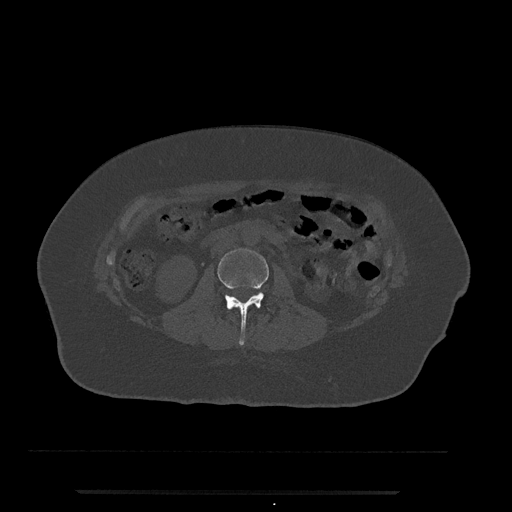
CT including the spine, one axial slice. Slice 30 of 797 in the series (ordered by position). Reconstruction kernel Br40s/3. 120 kVp. Bone window (W 1800 / L 400 HU). 512 × 512 image matrix, field of view 440 × 440 mm. Female patient, age 51 years. From the clinical record (not read from this slice): primary cancer: neuro.
Annotated regions visible in this slice (semi-automatic segmentation, software-assisted and operator-edited):
- L2 vertebra: box from (x=218, y=248) to (x=269, y=345) px